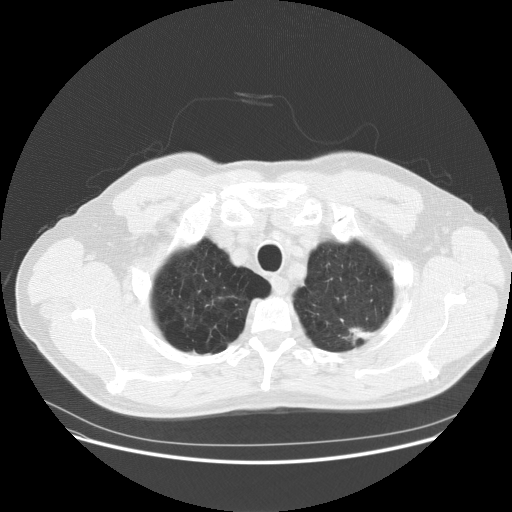
Low-dose screening chest CT, one axial slice; slice 145 of 158 in the series (ordered by position); reconstruction kernel STANDARD; 120 kVp; lung window (W 1500 / L -600 HU); 2.5 mm slice thickness; 512 × 512 image matrix, field of view 400 × 400 mm.
Outlined on this slice (manually delineated by an expert):
- lesion 1 (tumor, upper lobe of left lung): bounding box [x1, y1, x2, y2] px = [344, 327, 378, 344]